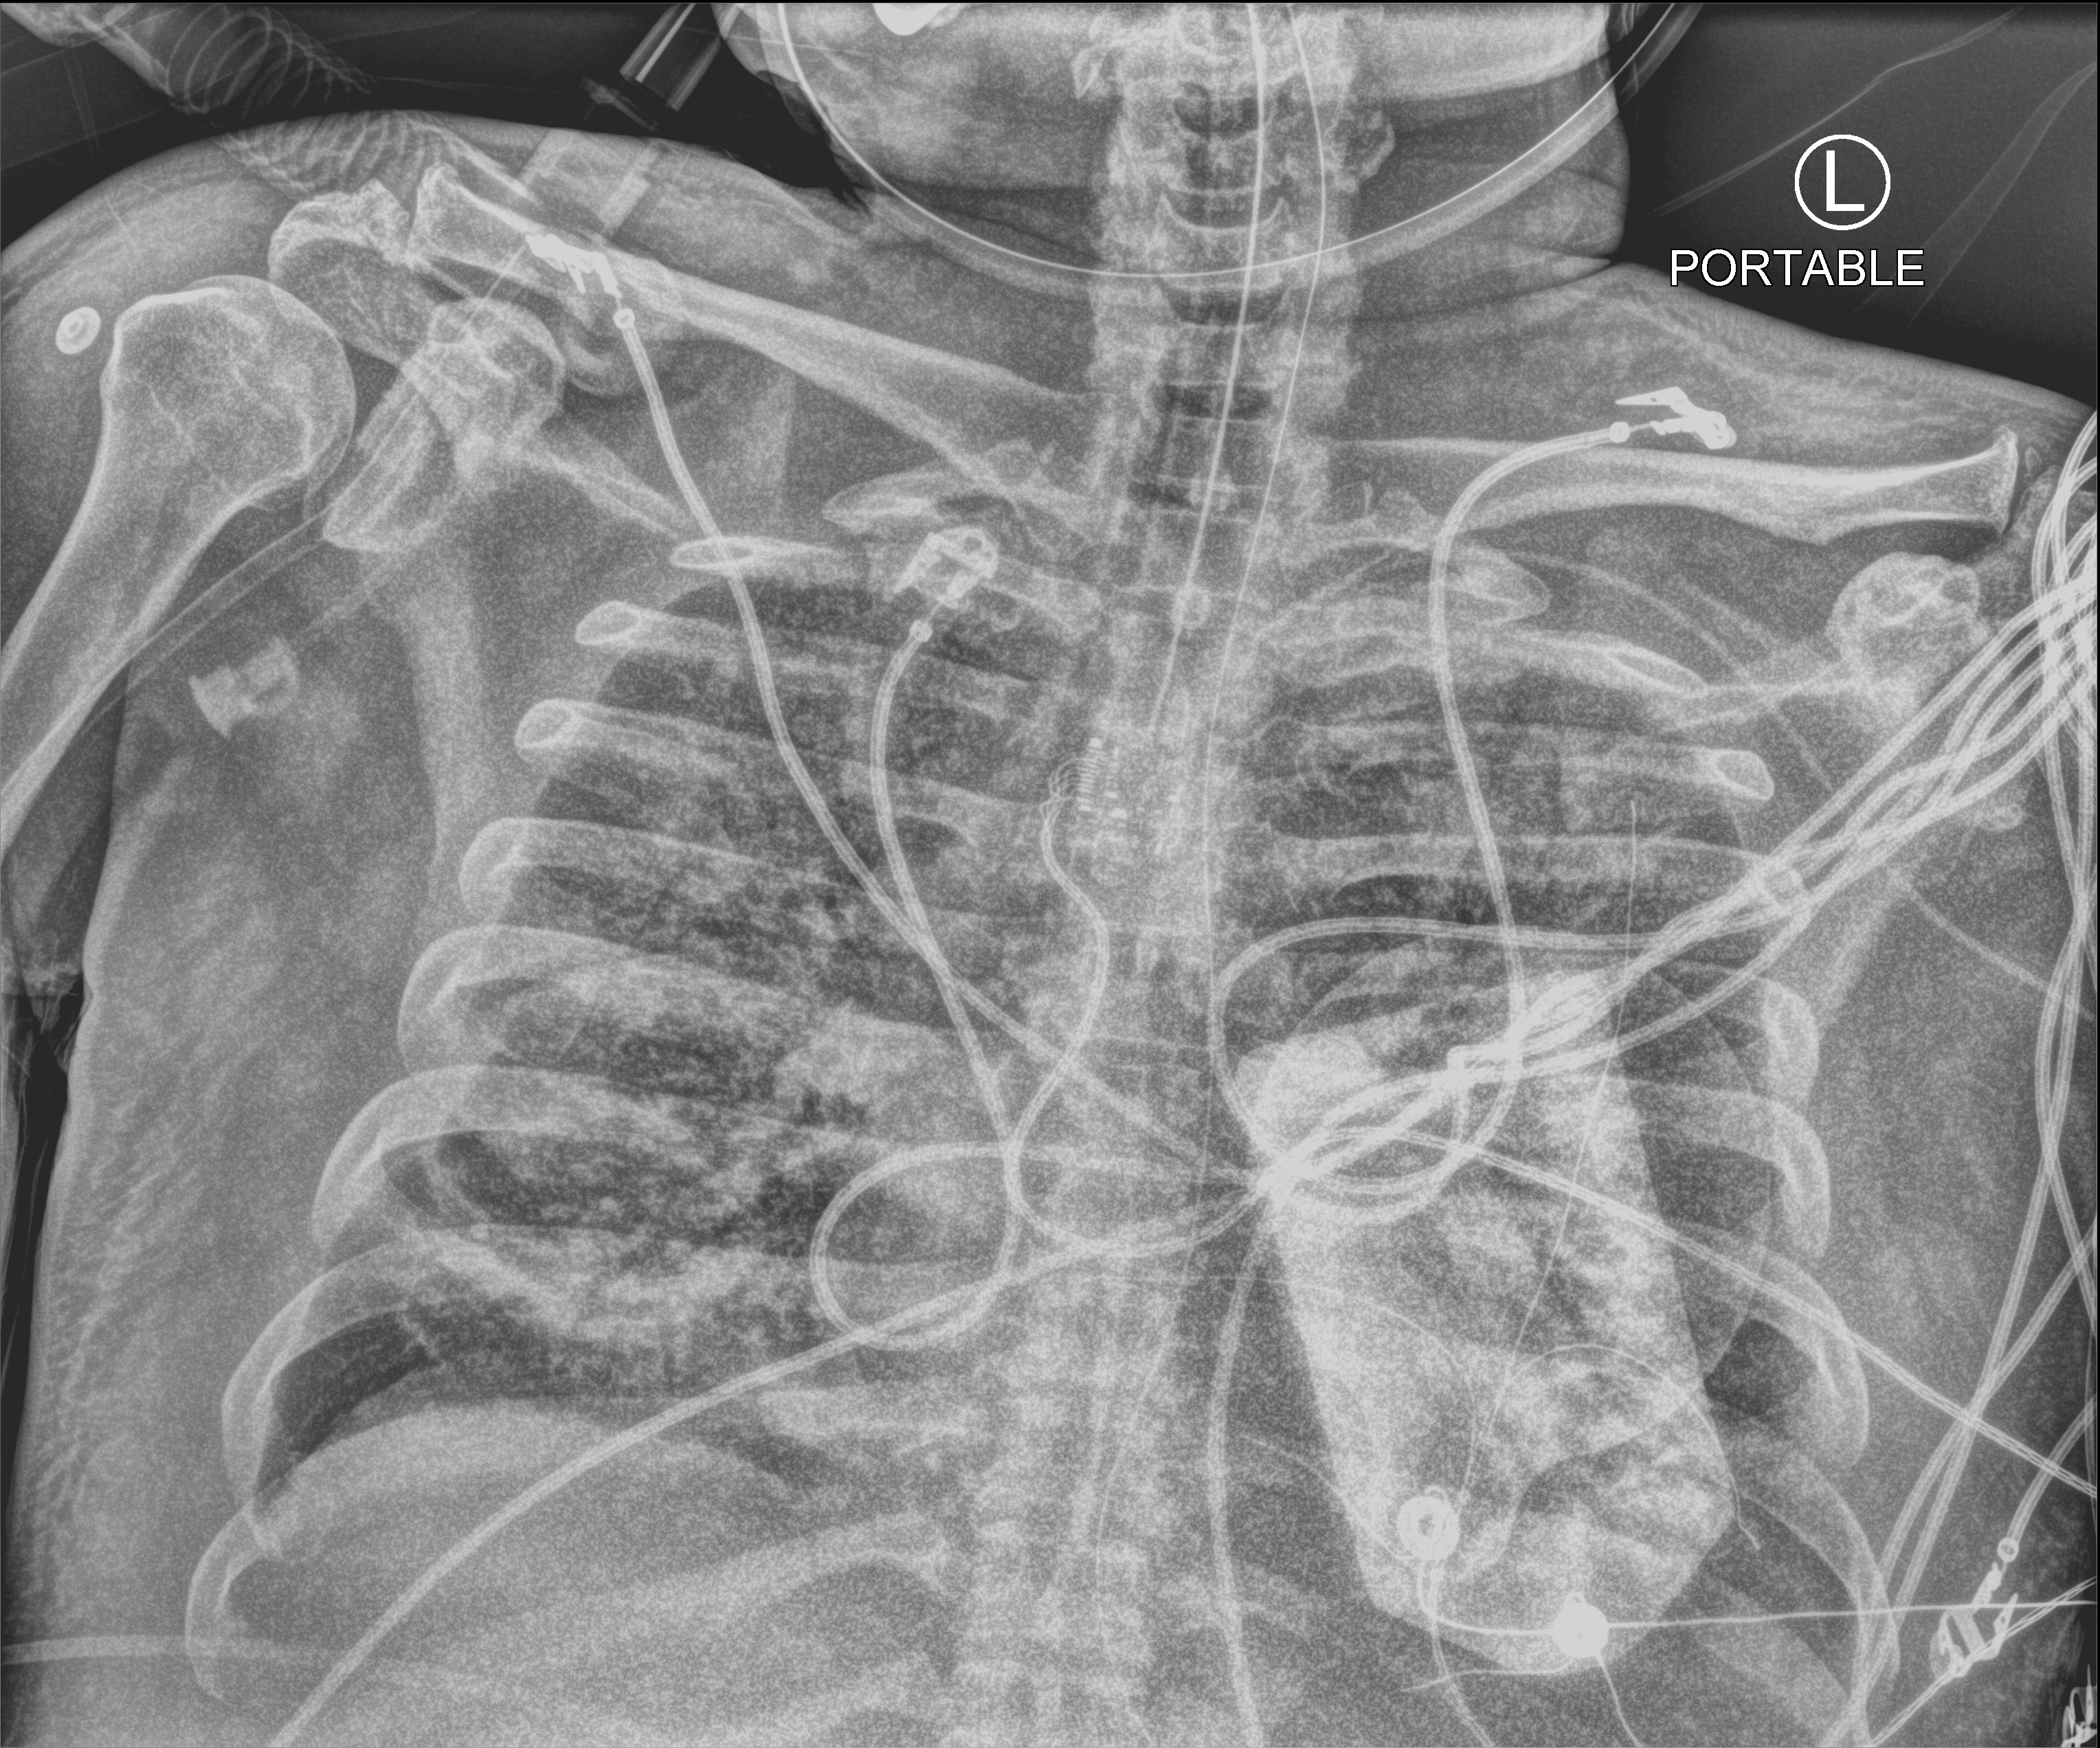
Bedside chest radiograph (computed radiography); anteroposterior (AP) projection. Patient hospitalised with COVID-19; male, aged 60–74 years.
Admission-level facts for this patient (not findings on this image; timing relative to this image not recorded): admitted to intensive care during this hospital stay: yes.